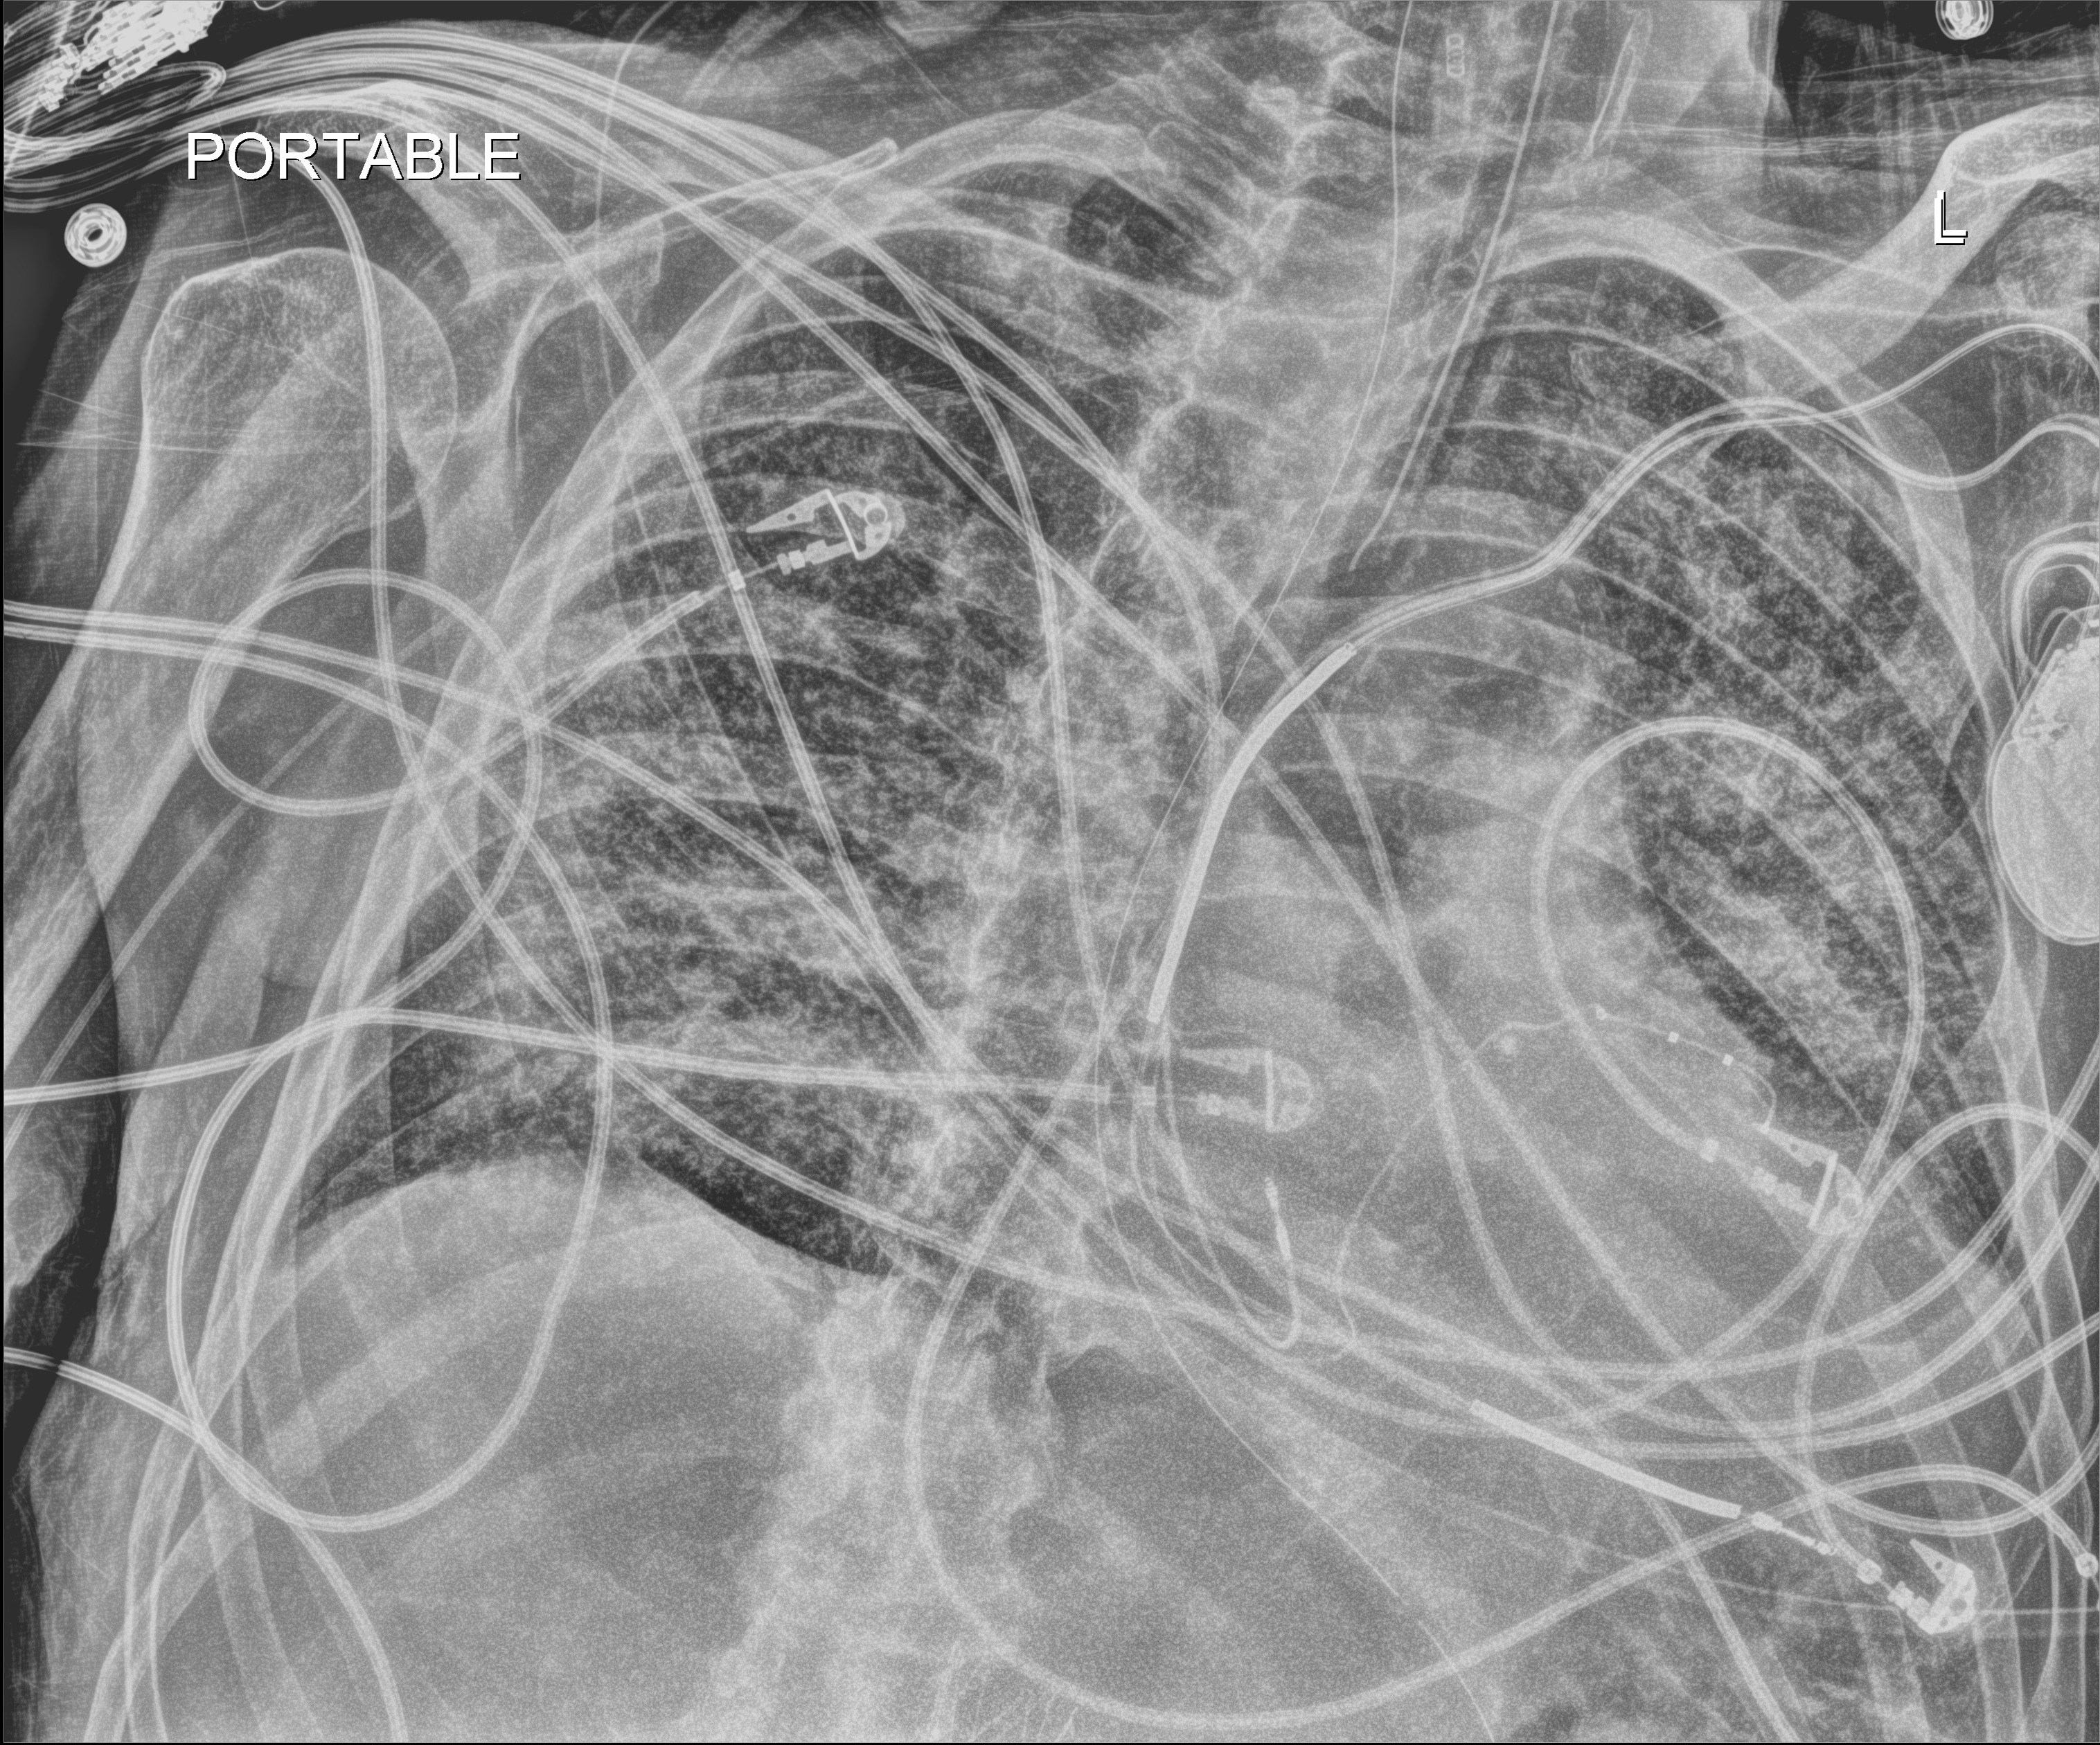
Portable chest radiograph; anteroposterior (AP) projection. Patient hospitalised with COVID-19; male, aged 60–74 years.
From the hospital-stay record, not from the radiograph (when in the stay this image was taken is not recorded): admitted to intensive care during this hospital stay: yes; mechanically ventilated during this hospital stay: yes.